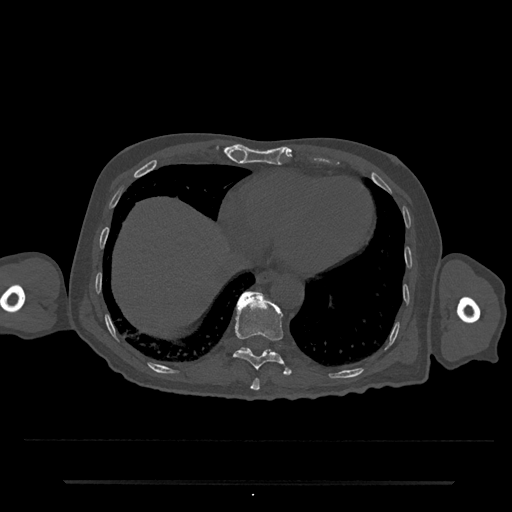
CT including the spine, one axial slice; position 307 of 797 along the scan axis; reconstruction kernel Br40s/3; 120 kVp; bone window (W 1800 / L 400 HU); 0.5 mm slice thickness; 512 × 512 image matrix. Male patient, age 74 years. Case-level facts recorded for this patient, not image findings: primary cancer: prostate.
Annotated regions visible in this slice (semi-automatically segmented with operator editing):
- T10 vertebra: bounding box <233,292,292,376> (left, top, right, bottom; pixels)
- T11 vertebra: <240,292,262,350>
- T9 vertebra: <250,379,260,391>